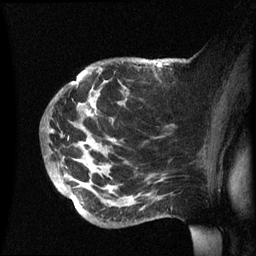
Breast MRI (dynamic contrast-enhanced), one sagittal slice; slice 41 of 60 in the series (ordered by position); dynamic contrast-enhanced series, image 2 of 3 at this slice position (ordered by acquisition); 1.5 T; TE 4.2 ms, TR 8.4 ms; 2.4 mm slice thickness; 256 × 256 image matrix, field of view 230 × 230 mm. Female patient, age 49 years.
Structures marked on this image (semi-automatic segmentation, software-assisted and operator-edited):
- analysis volume of interest (the breast-tissue region the enhancement analysis was run in; not a lesion): bounding box (x1, y1, x2, y2) in pixels: (43, 58, 174, 227)
- tumour enhancement mask (voxels above the 70 % enhancement threshold inside the analysis volume of interest): (157, 62, 162, 67)